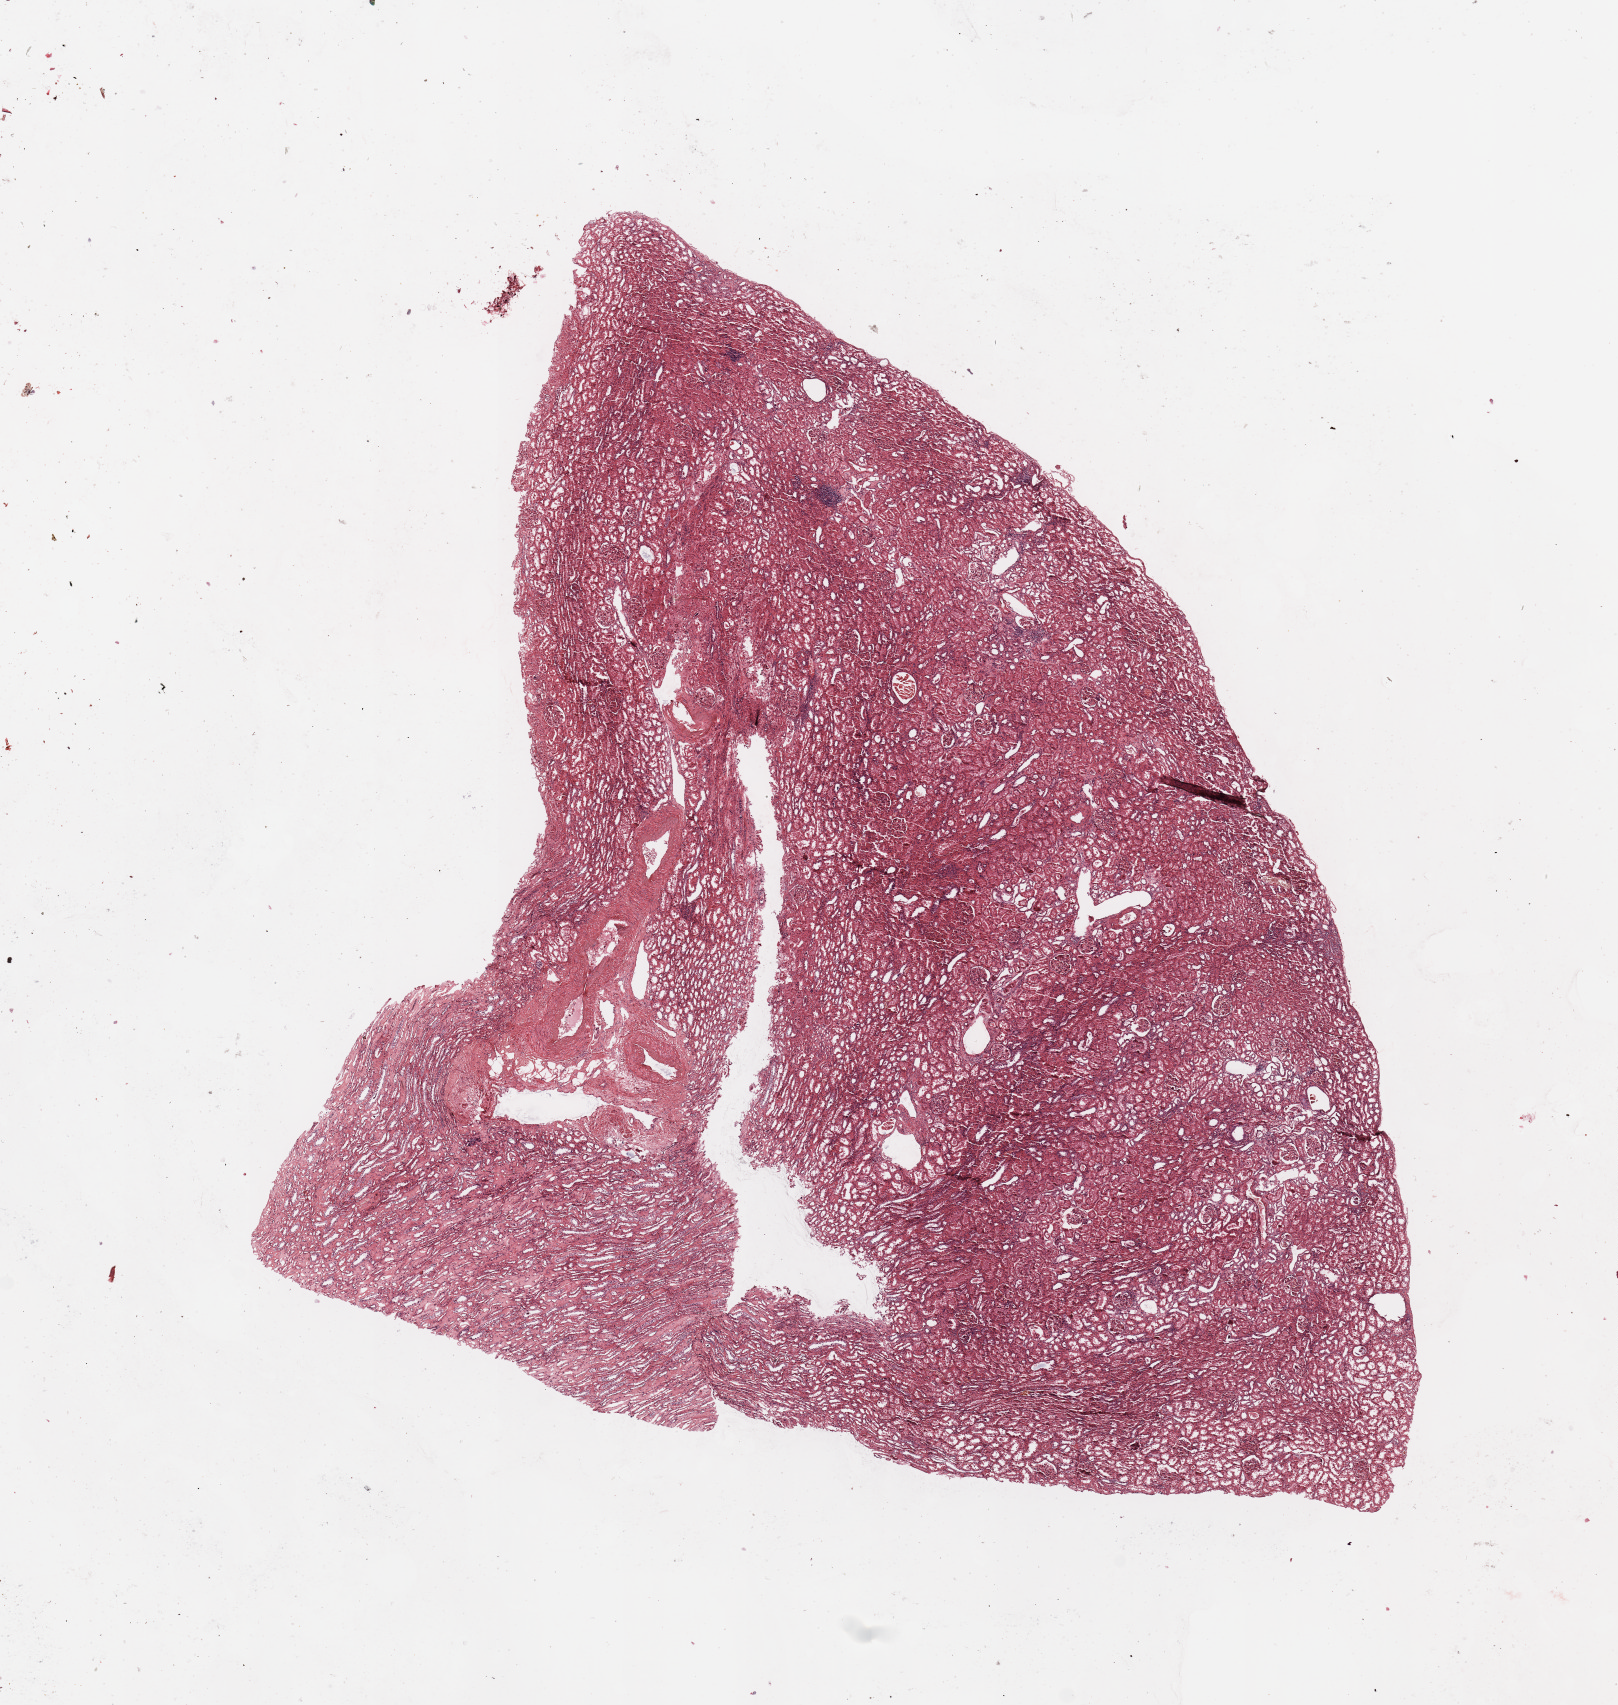
Digitized H&E-stained tissue section (whole slide) — whole scanned area (about 12.8 x 13.5 mm, slide scanned at 20x) shown as a low-resolution overview. Normal (non-tumour) tissue sample, sampled site: kidney. 65-year-old male patient.
This section: normal (non-tumour) tissue from the same patient. Patient diagnosis: Renal cell carcinoma, NOS.